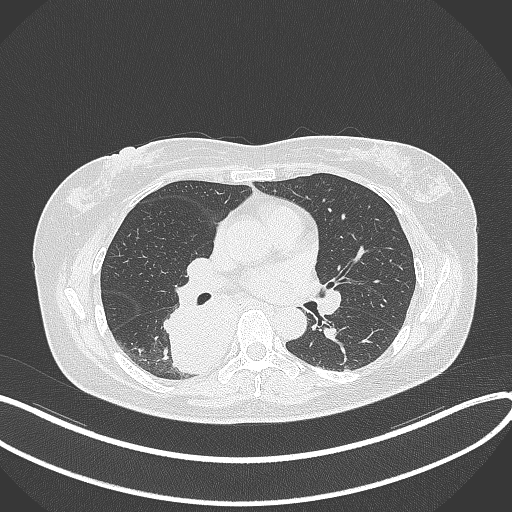
Chest CT, one axial slice. Position 195 of 331 along the scan axis. Reconstruction kernel B70f. Lung window (W 1500 / L -600 HU). 1 mm slice thickness. 512 × 512 image matrix, field of view 400 × 400 mm. Patient: female, 54 years. Case-level facts recorded for this patient, not image findings: clinical TNM (as recorded): T4 N0 M0.
Annotated regions visible in this slice (rectangle marked by the reading radiologist):
- lung tumour (recorded histology: adenocarcinoma): bounding box (x1, y1, x2, y2) in pixels: (161, 291, 240, 375)